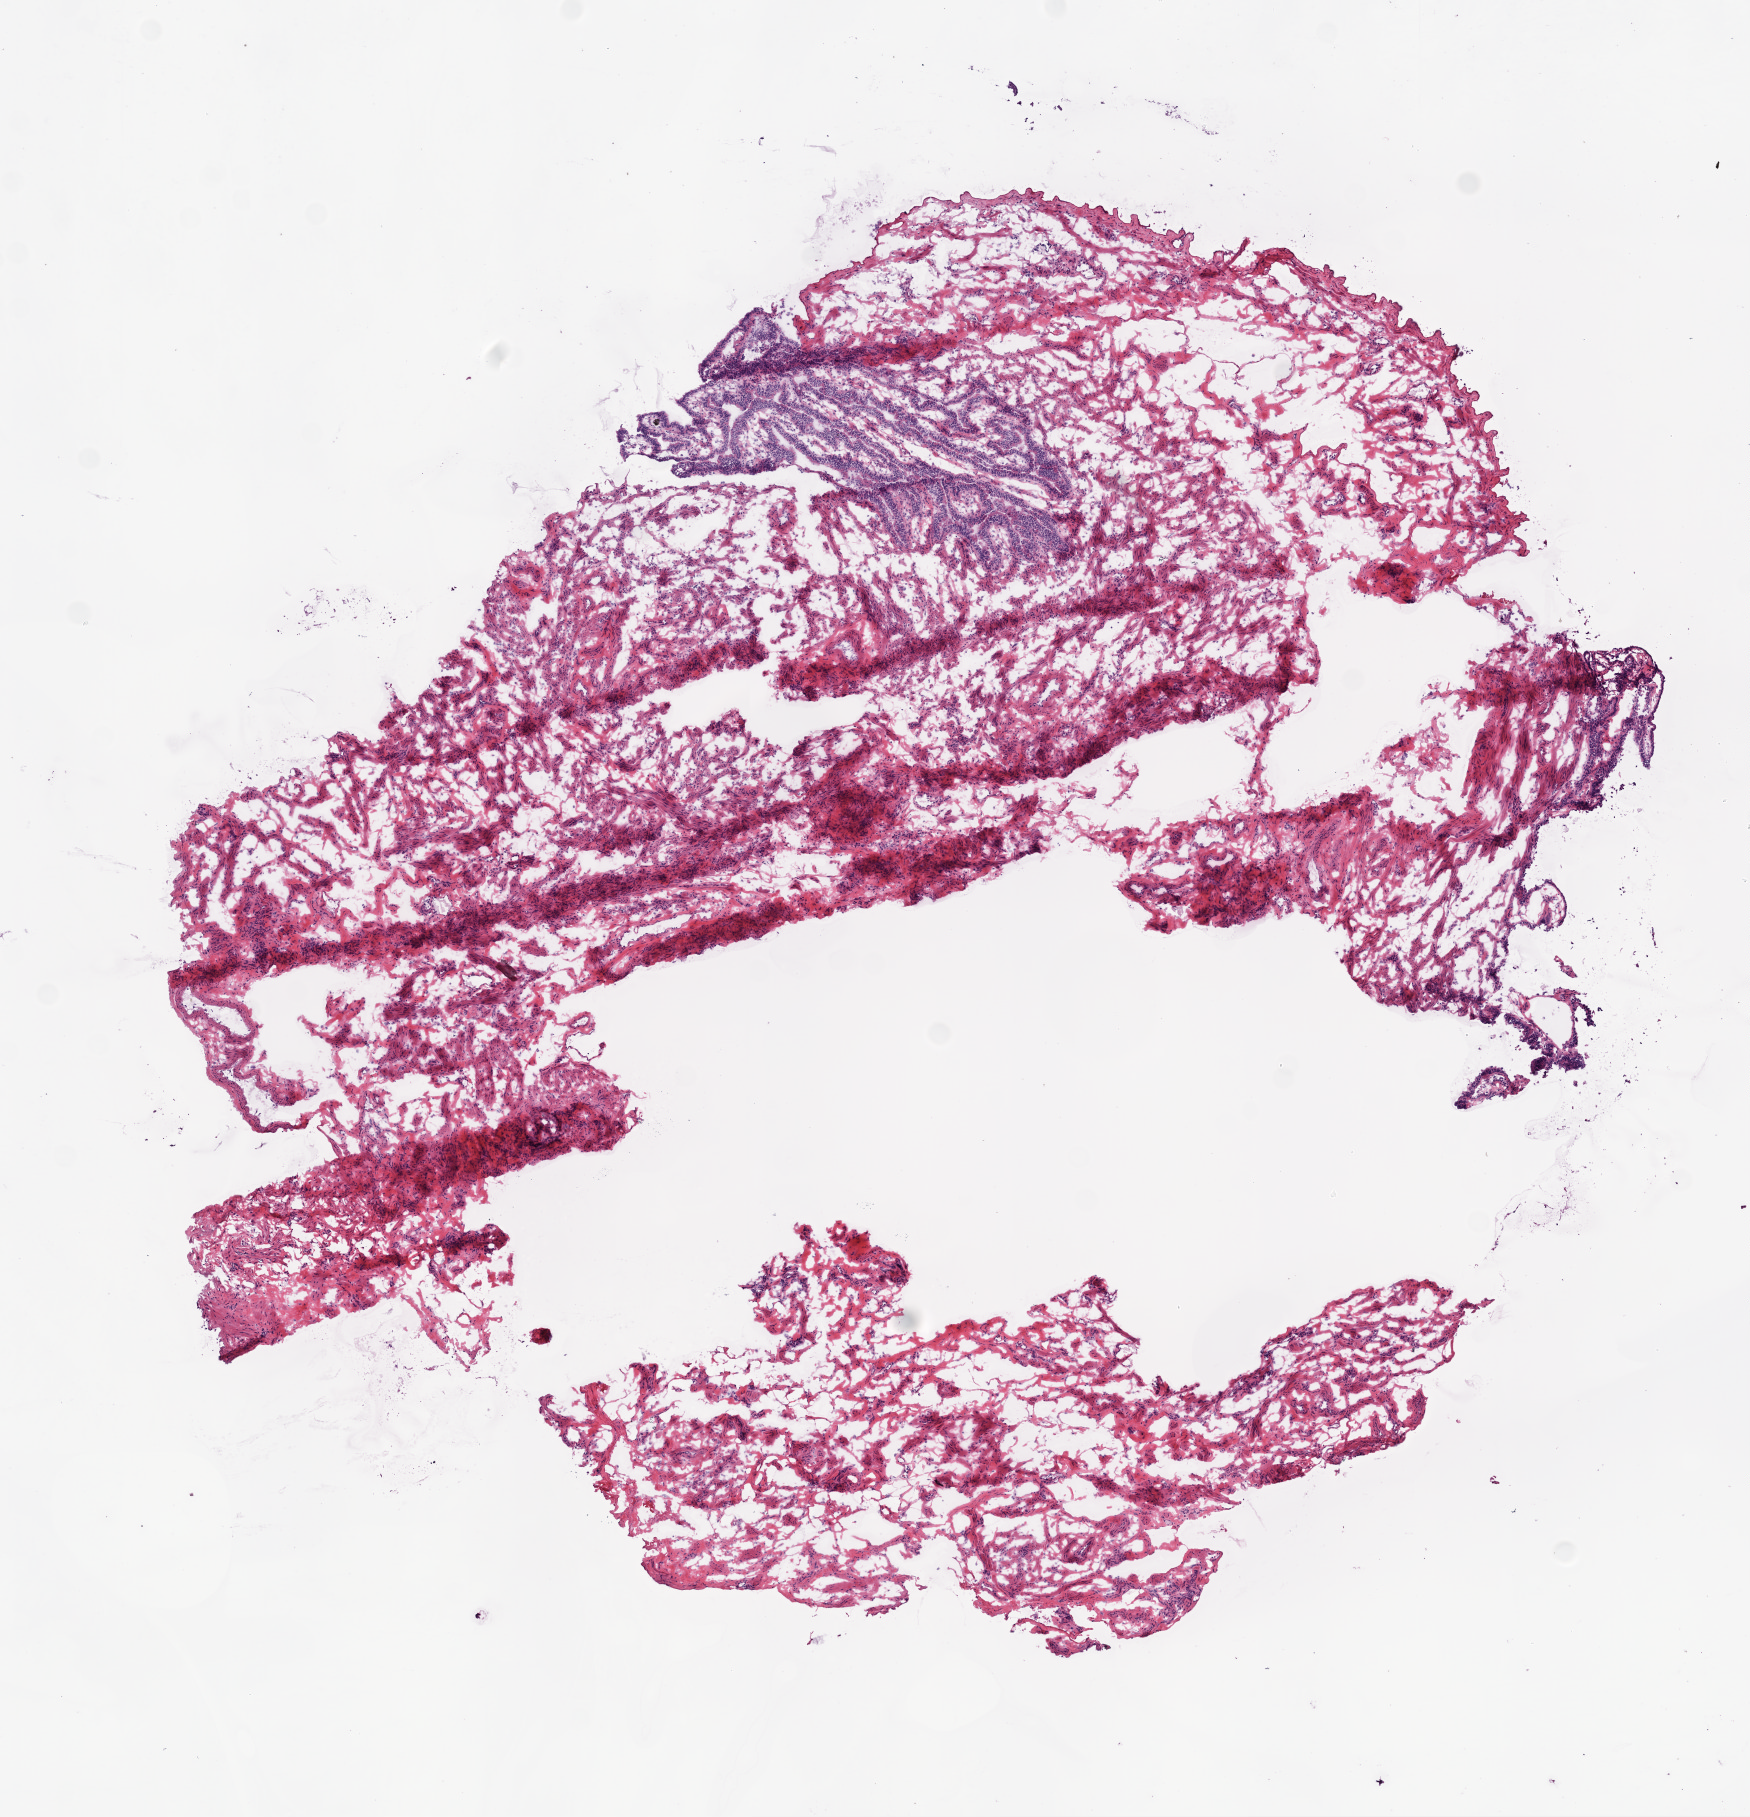
Whole-slide histology image, Hematoxylin and eosin (H&E) stained — shown as a low-resolution overview of the whole scanned area (about 7.0 x 7.3 mm, slide scanned at 20x). Frozen section from the bottom of the tissue portion. Sample: solid tissue normal (non-tumour tissue), ovary. Patient: female, age at initial diagnosis 40 years.
This section: solid tissue normal (non-tumour) sample from the same patient. Patient diagnosis: Serous cystadenocarcinoma, NOS.